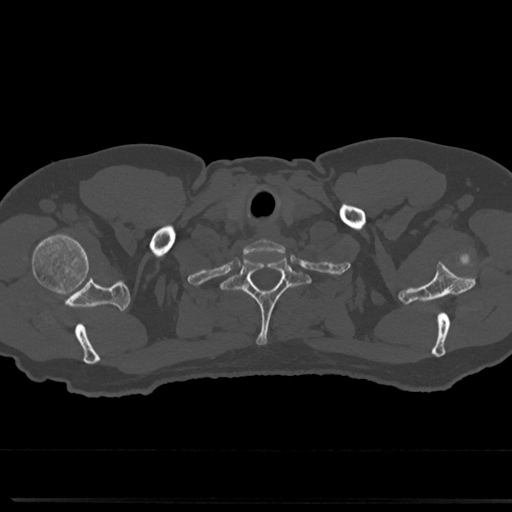
CT including the spine, one axial slice. Position 677 of 817 along the scan axis. 120 kVp. Bone window (W 1800 / L 400 HU). 0.5 mm slice thickness. 512 × 512 image matrix. Patient: male, 61 years. From the clinical record (not read from this slice): primary cancer: prostate.
Annotated regions visible in this slice (semi-automatically segmented with operator editing):
- T1 vertebra: bounding box (x1, y1, x2, y2) in pixels: (229, 251, 304, 347)
- T2 vertebra: (212, 292, 315, 313)